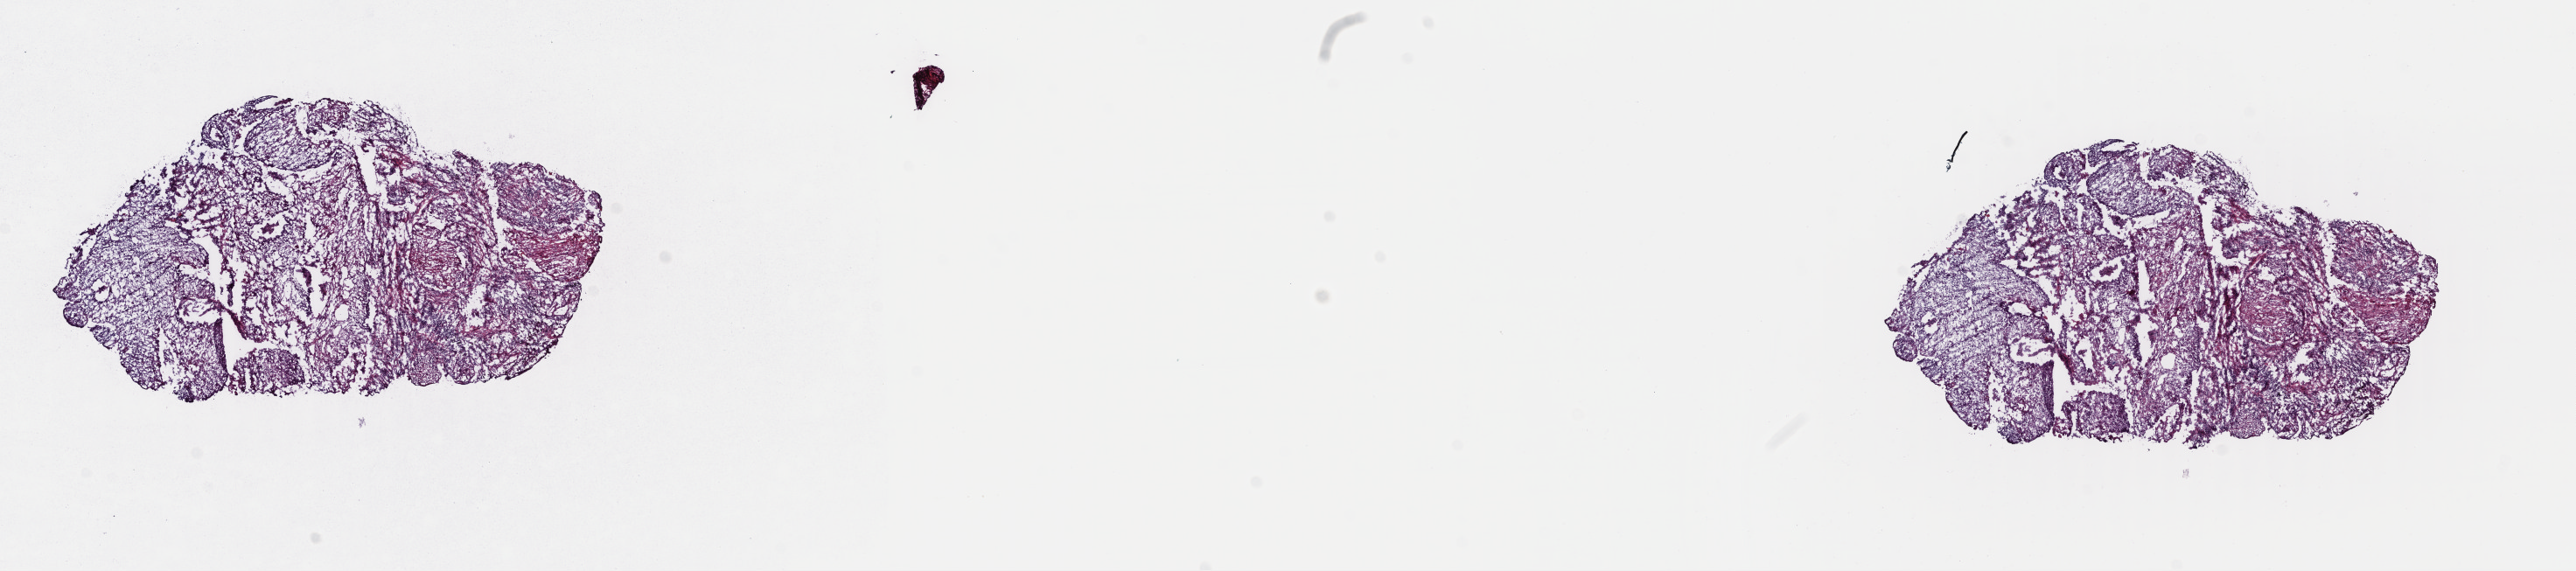
Digitized H&E tissue section (whole slide), whole scanned area (about 23.1 x 5.1 mm, from a 40x scan) shown as a low-resolution overview, frozen section from the top of the tissue portion, lung, primary tumour sample. Male patient; age at initial diagnosis 77 years. Composition of this section per pathologist review: tumour cells 90%, tumour nuclei 90%.
Histologic diagnosis: Squamous cell carcinoma, NOS (upper lobe, lung).